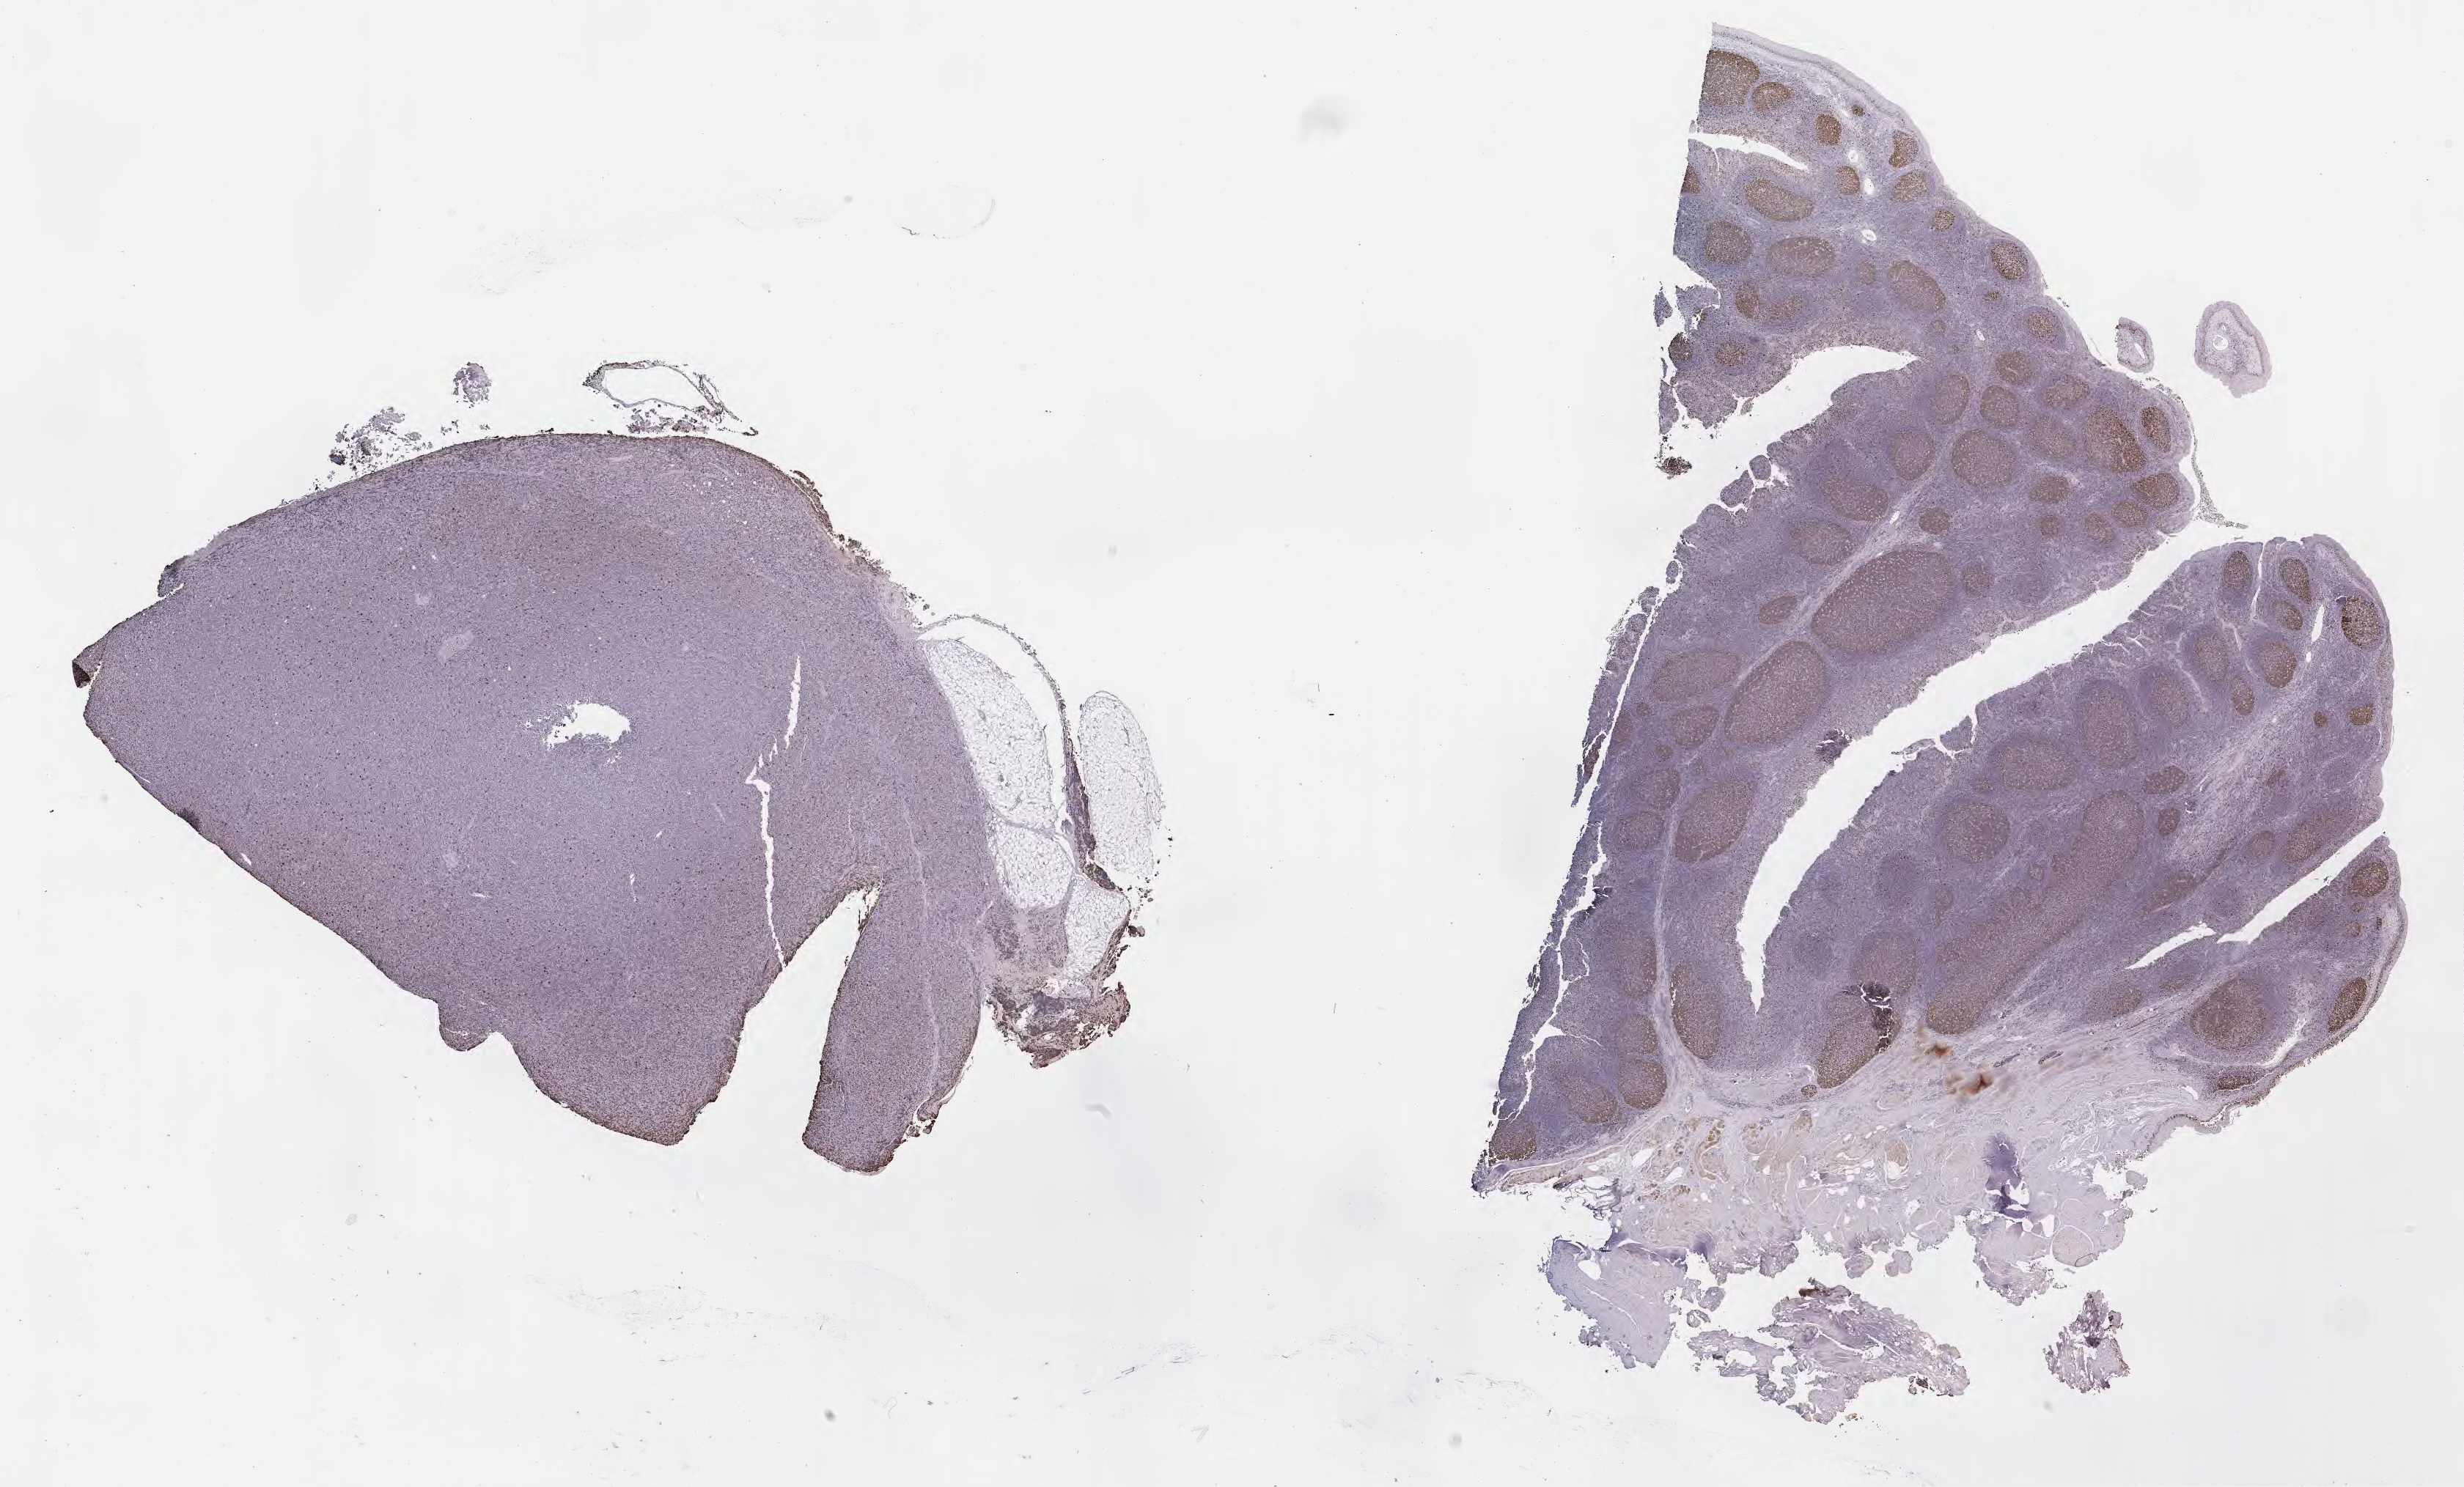
Immunohistochemistry (IHC) whole-slide image stained for Ki-67, whole scanned area (about 27.2 x 16.4 mm) shown as a low-resolution overview; specimen: tumor tissue; anatomic site: lymph node. Patient: male, aged 26.
• histologic diagnosis: Diffuse large B-cell lymphoma, NOS